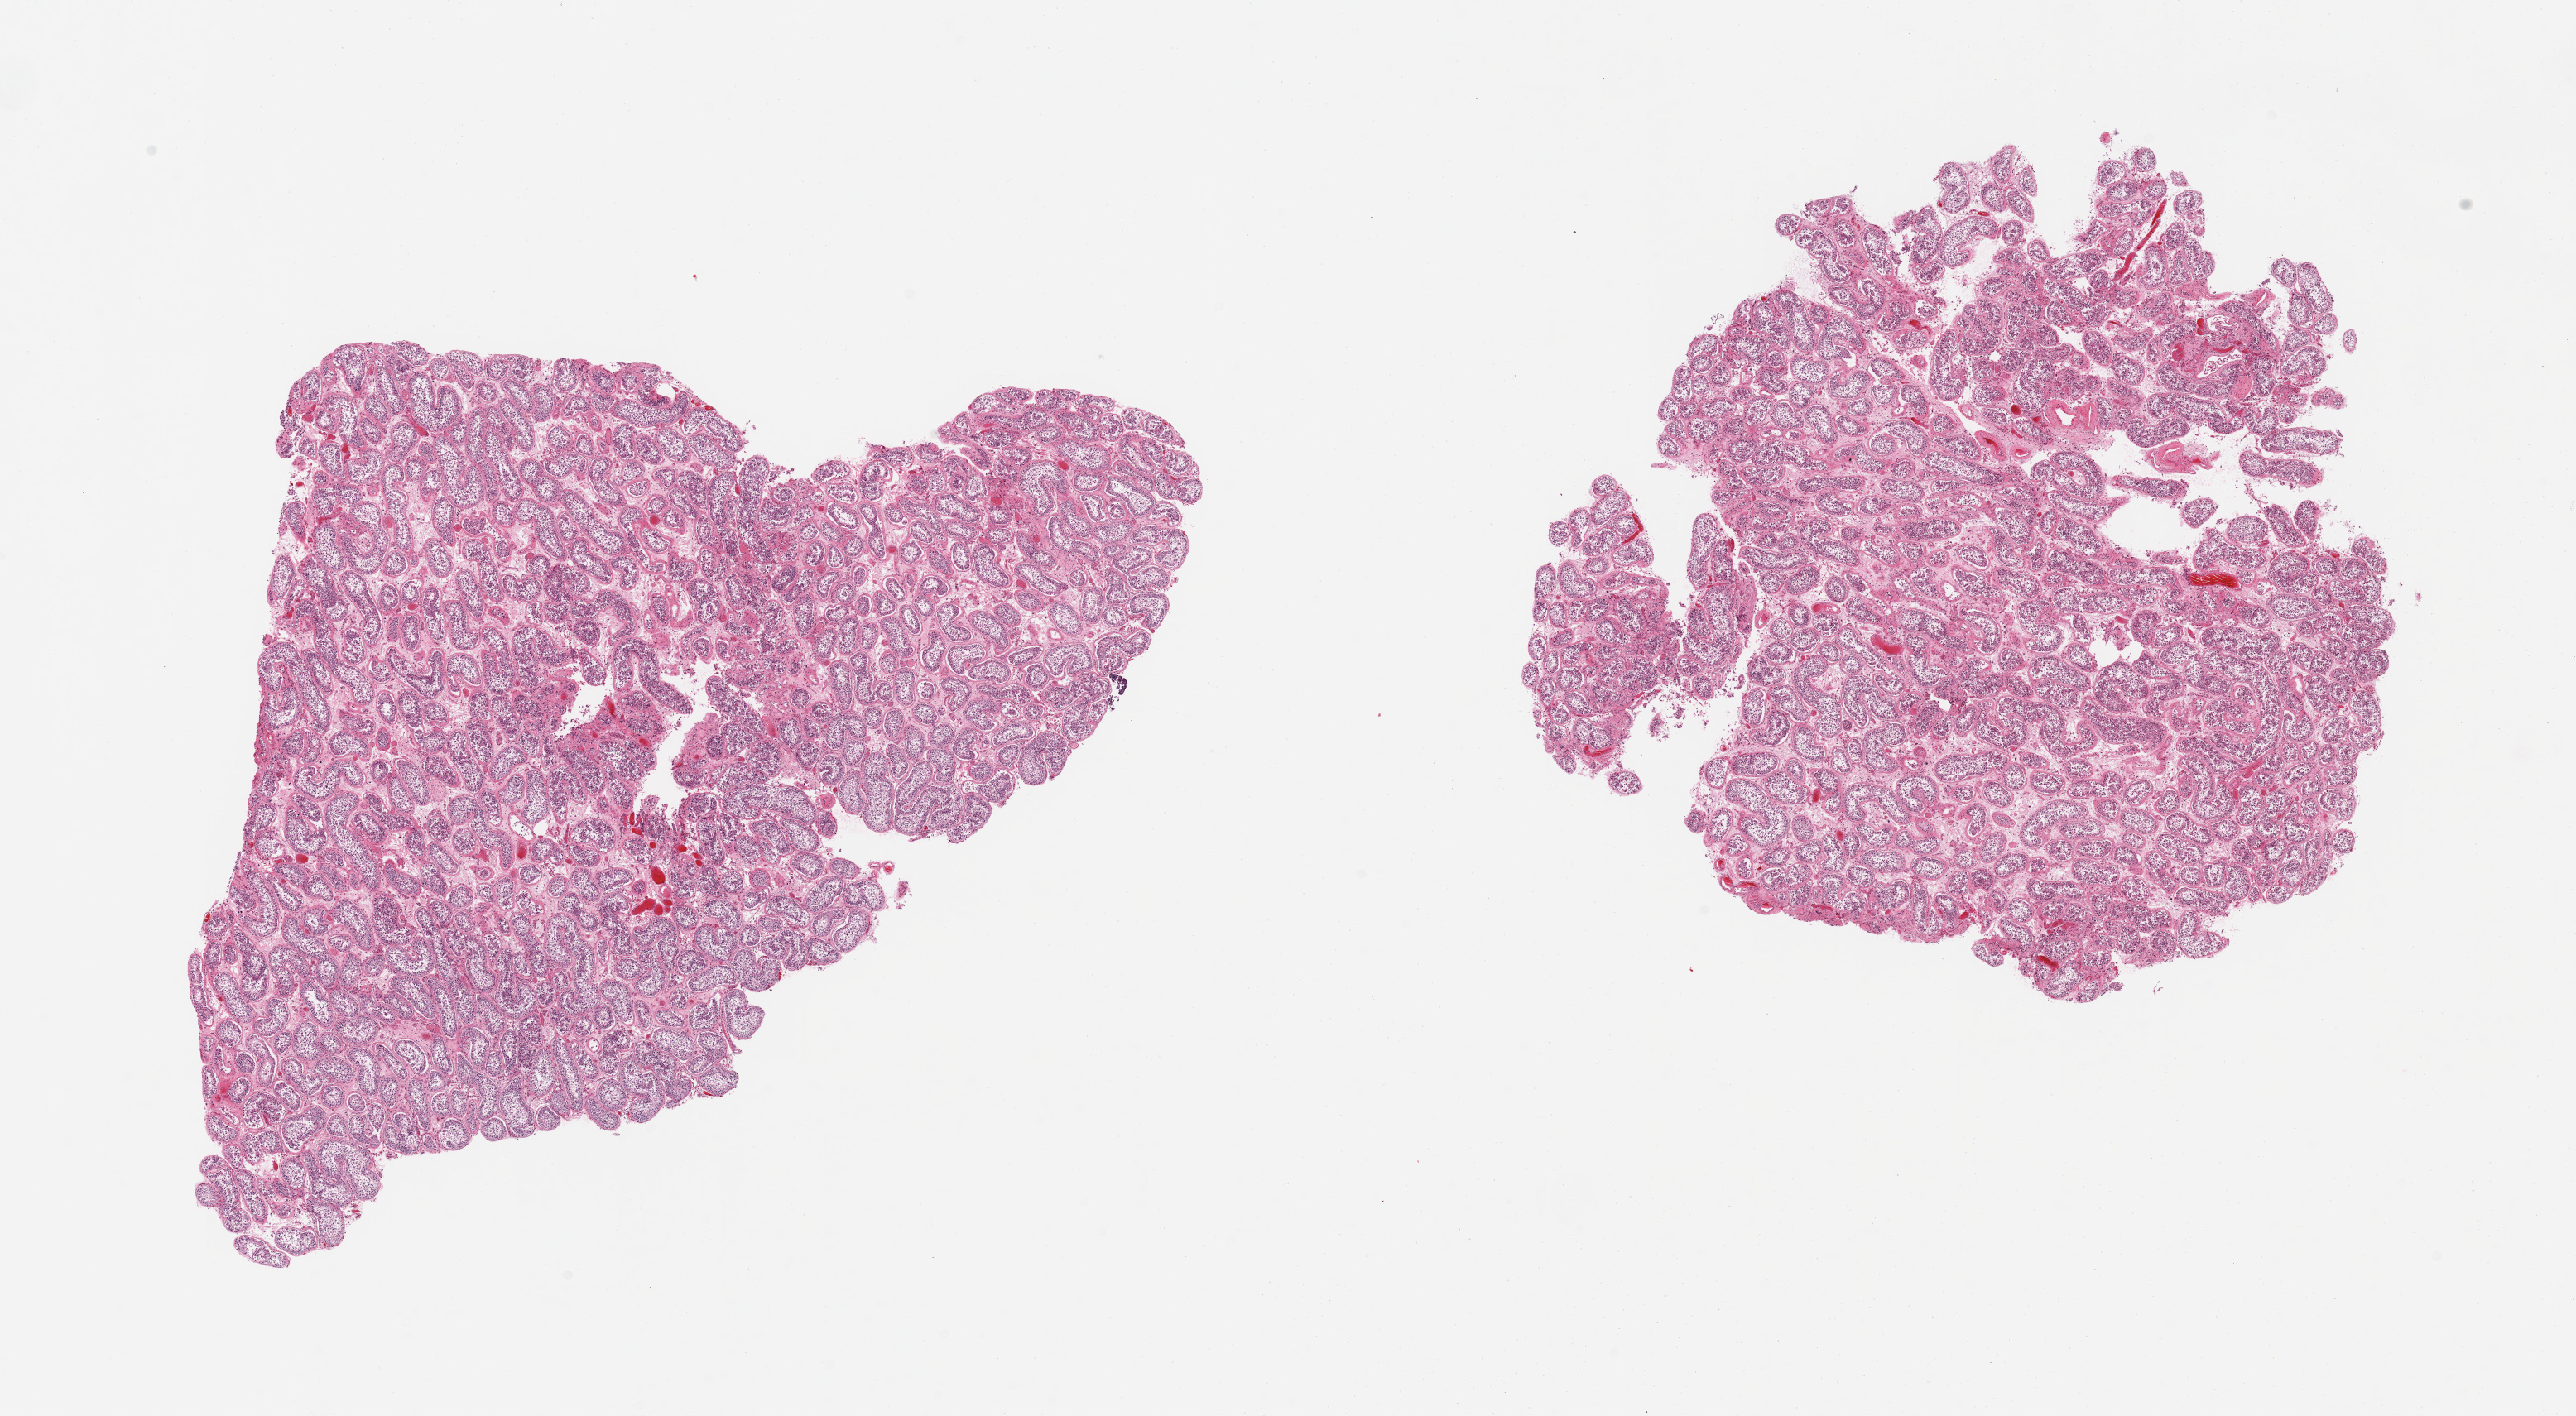
Haematoxylin and eosin whole-slide image, low-resolution overview of the scanned area, about 24.6 x 13.5 mm (slide scanned at 20x); PAXgene-fixed paraffin-embedded (PFPE) section; section of testis (target tissue); tissue donor sample. Donor sex: male.
* reviewer comment on this tissue sample: 2 pieces, spermatogenesis